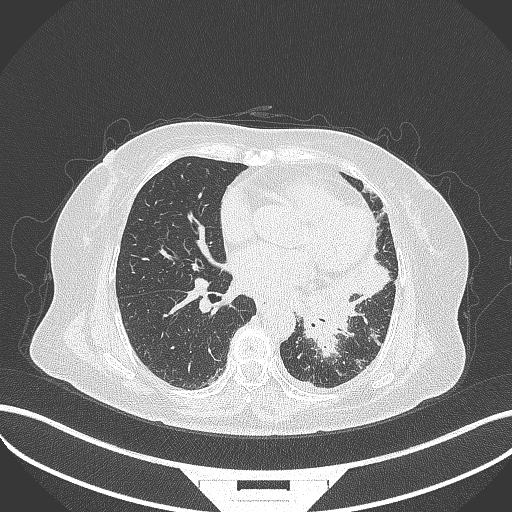
Chest CT, one axial slice. Position 158 of 322 along the scan axis. Reconstruction kernel B70f. Lung window (W 1500 / L -600 HU). 512 × 512 image matrix, field of view 400 × 400 mm. Patient: female, 69 years. From the clinical record (not read from this slice): clinical TNM (as recorded): T2b N3 M1.
Annotated regions visible in this slice (rectangle marked by the reading radiologist):
- lung tumour (recorded histology: adenocarcinoma): bounding box <293,271,362,356> (left, top, right, bottom; pixels)